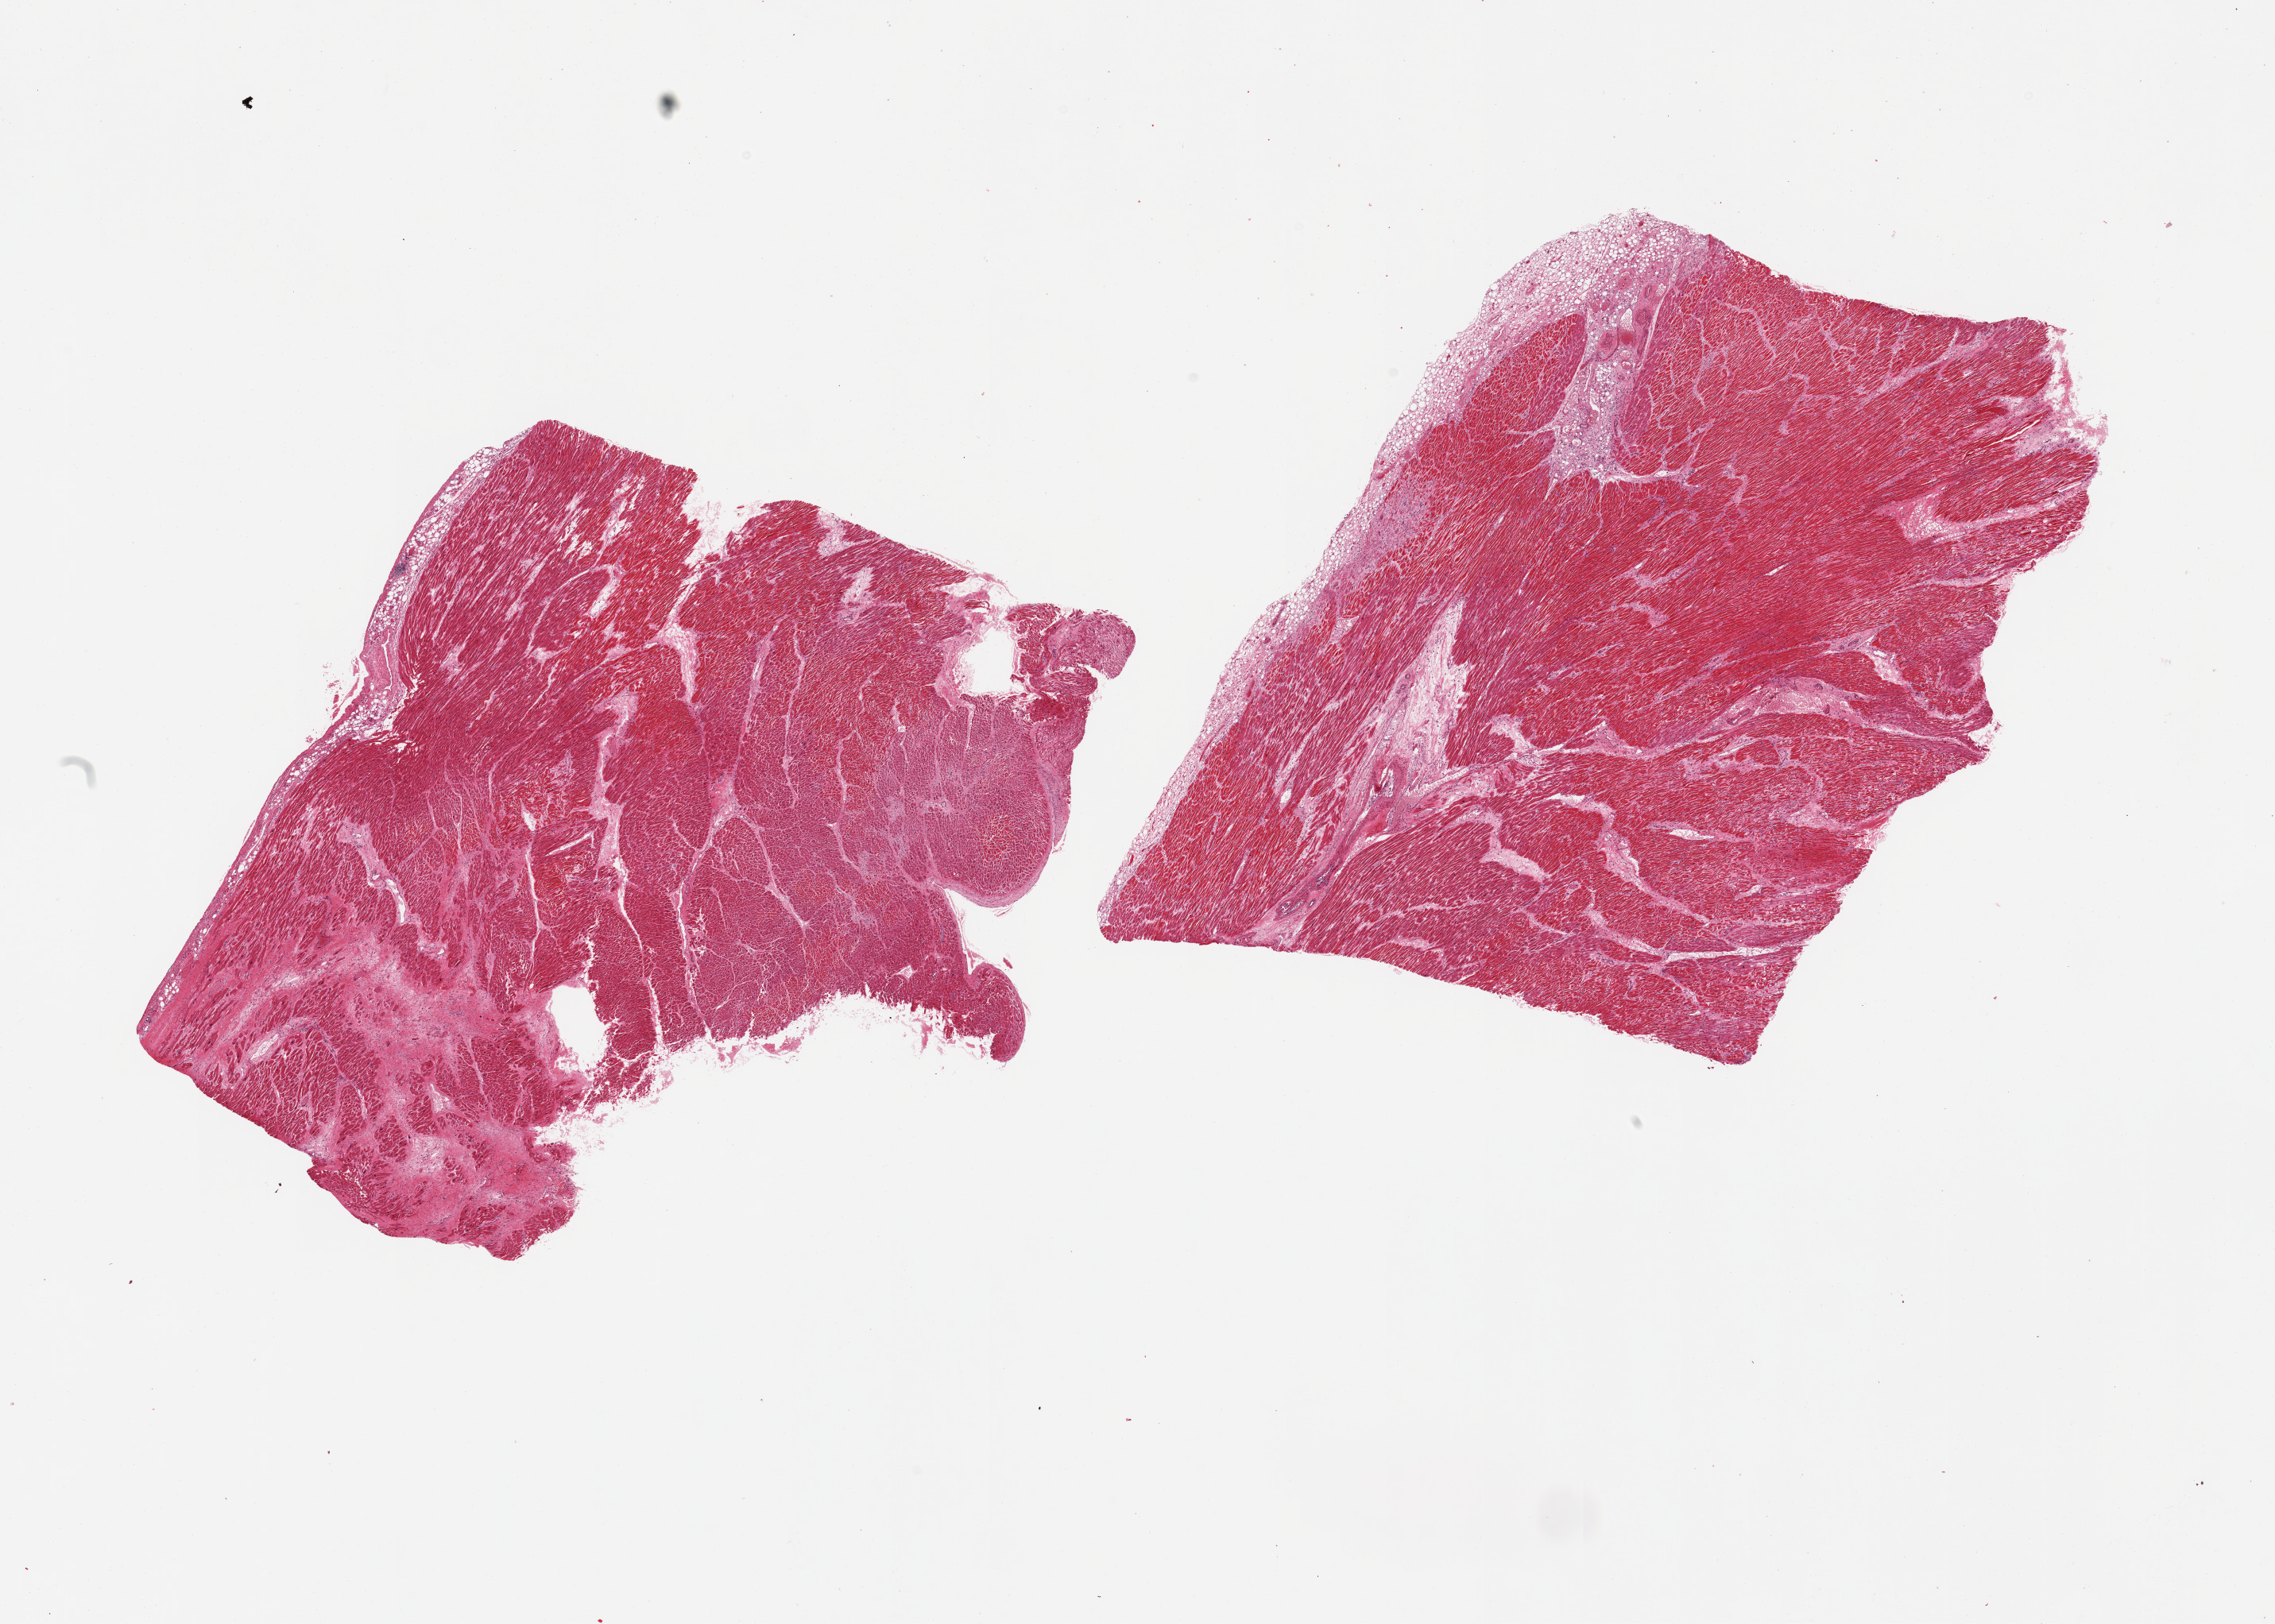
Hematoxylin and eosin (H&E) whole-slide image, a low-resolution overview of the entire scanned area, about 22.6 x 16.2 mm (from a 20x scan), PAXgene-fixed paraffin-embedded (PFPE) section, sampled site (target tissue): heart, tissue donor sample. Donor: male.
* review note (as recorded): 2 pieces; large and small areas of scarred and more recently damaged myocardium consistent with ischemia